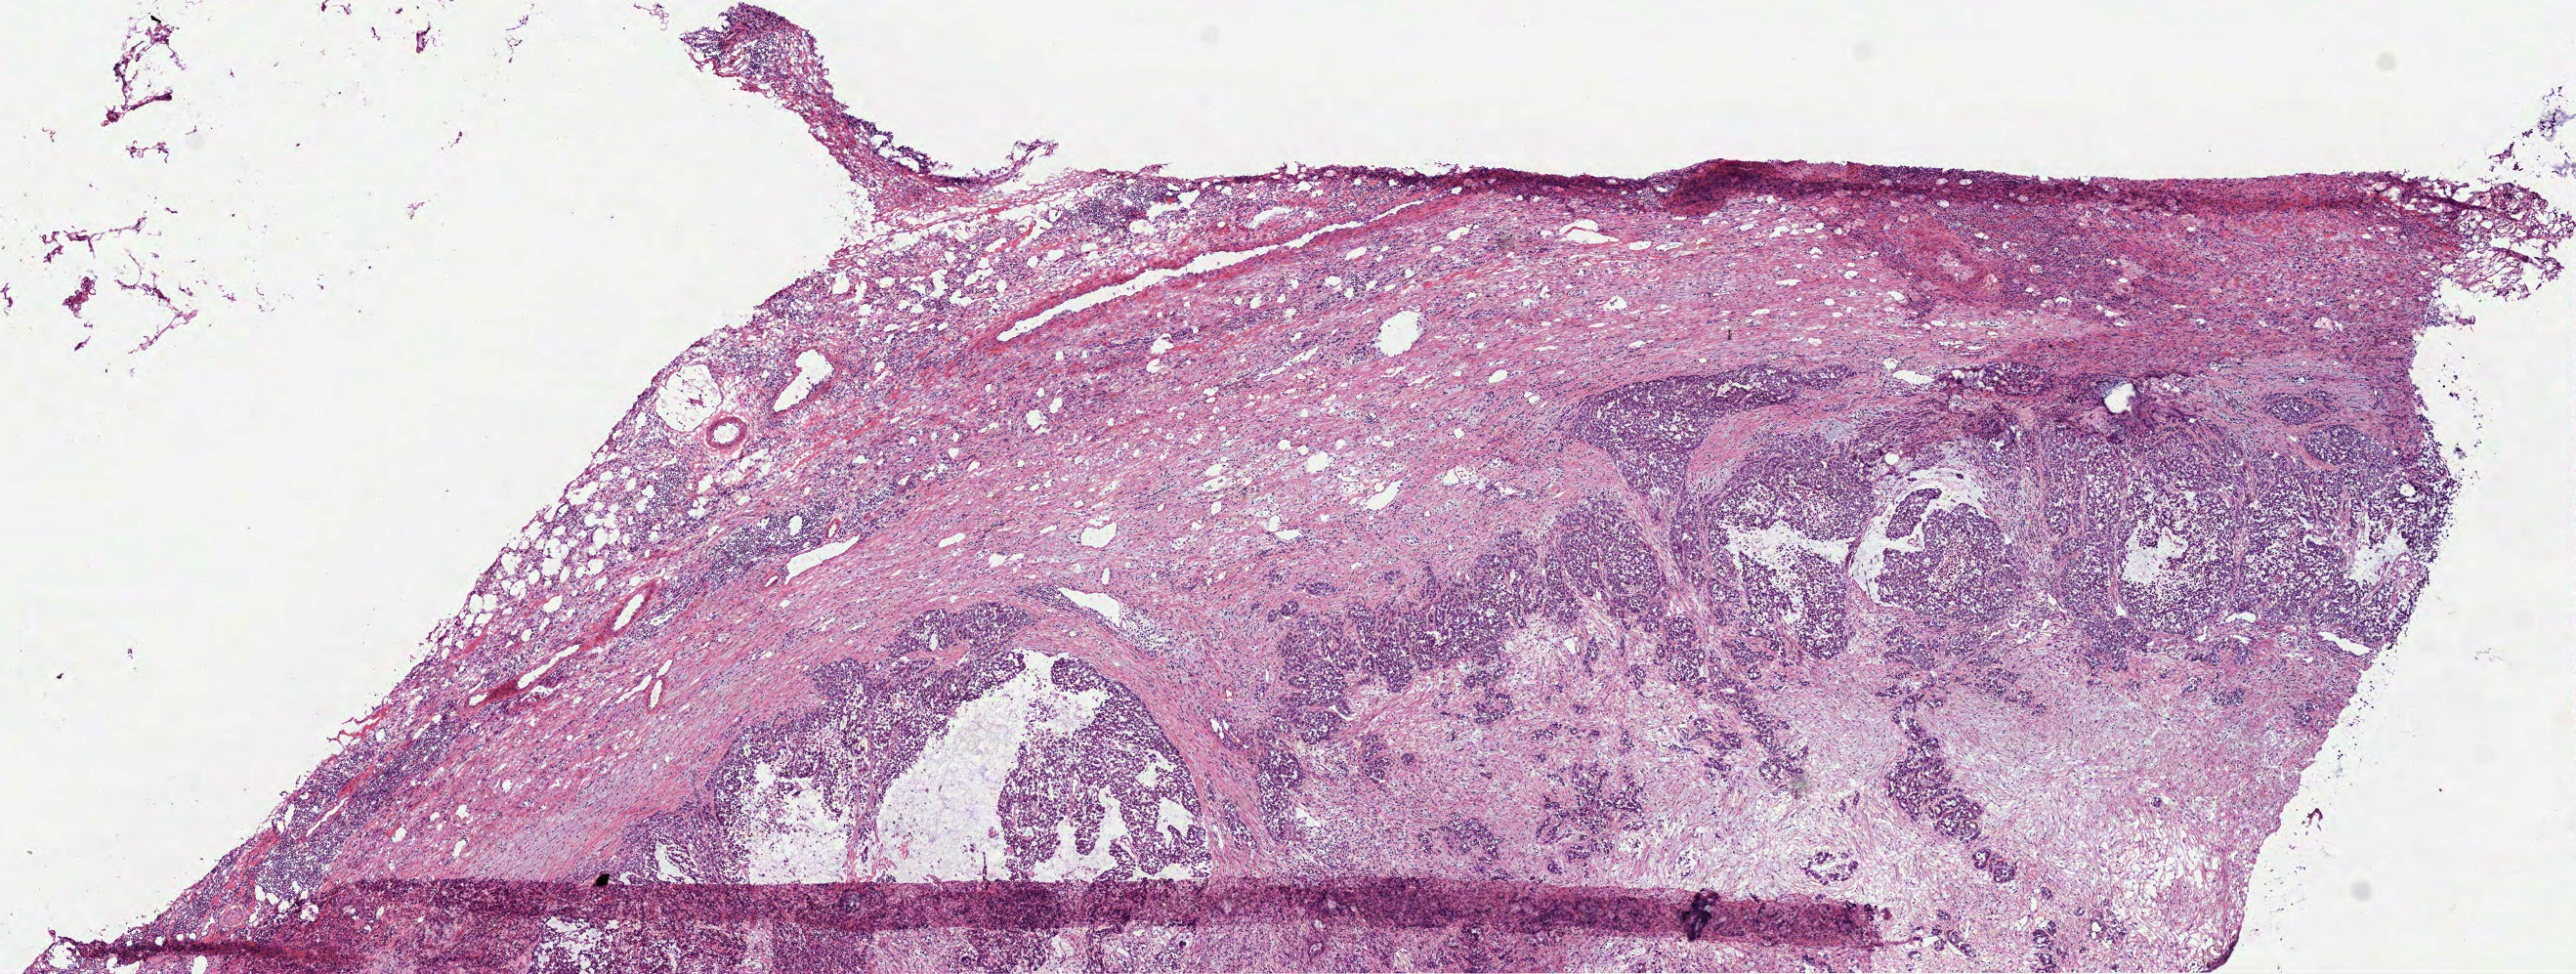
Digitized Hematoxylin and eosin (H&E) stained tissue section (whole slide) — low-resolution overview of the scanned area, about 10.6 x 4.0 mm, frozen section, colon, primary tumour sample. Male patient; age at initial diagnosis 47 years. Pathologist review of this section (percent, as recorded): tumour cells 40%, tumour nuclei 73%, normal cells 0%, stromal cells 60%, necrosis 0%.
• pathologic diagnosis: Mucinous adenocarcinoma (ascending colon)
• AJCC pathologic stage: IIIC (7th edition)
• lymph nodes positive (case pathology): 12 of 14 examined